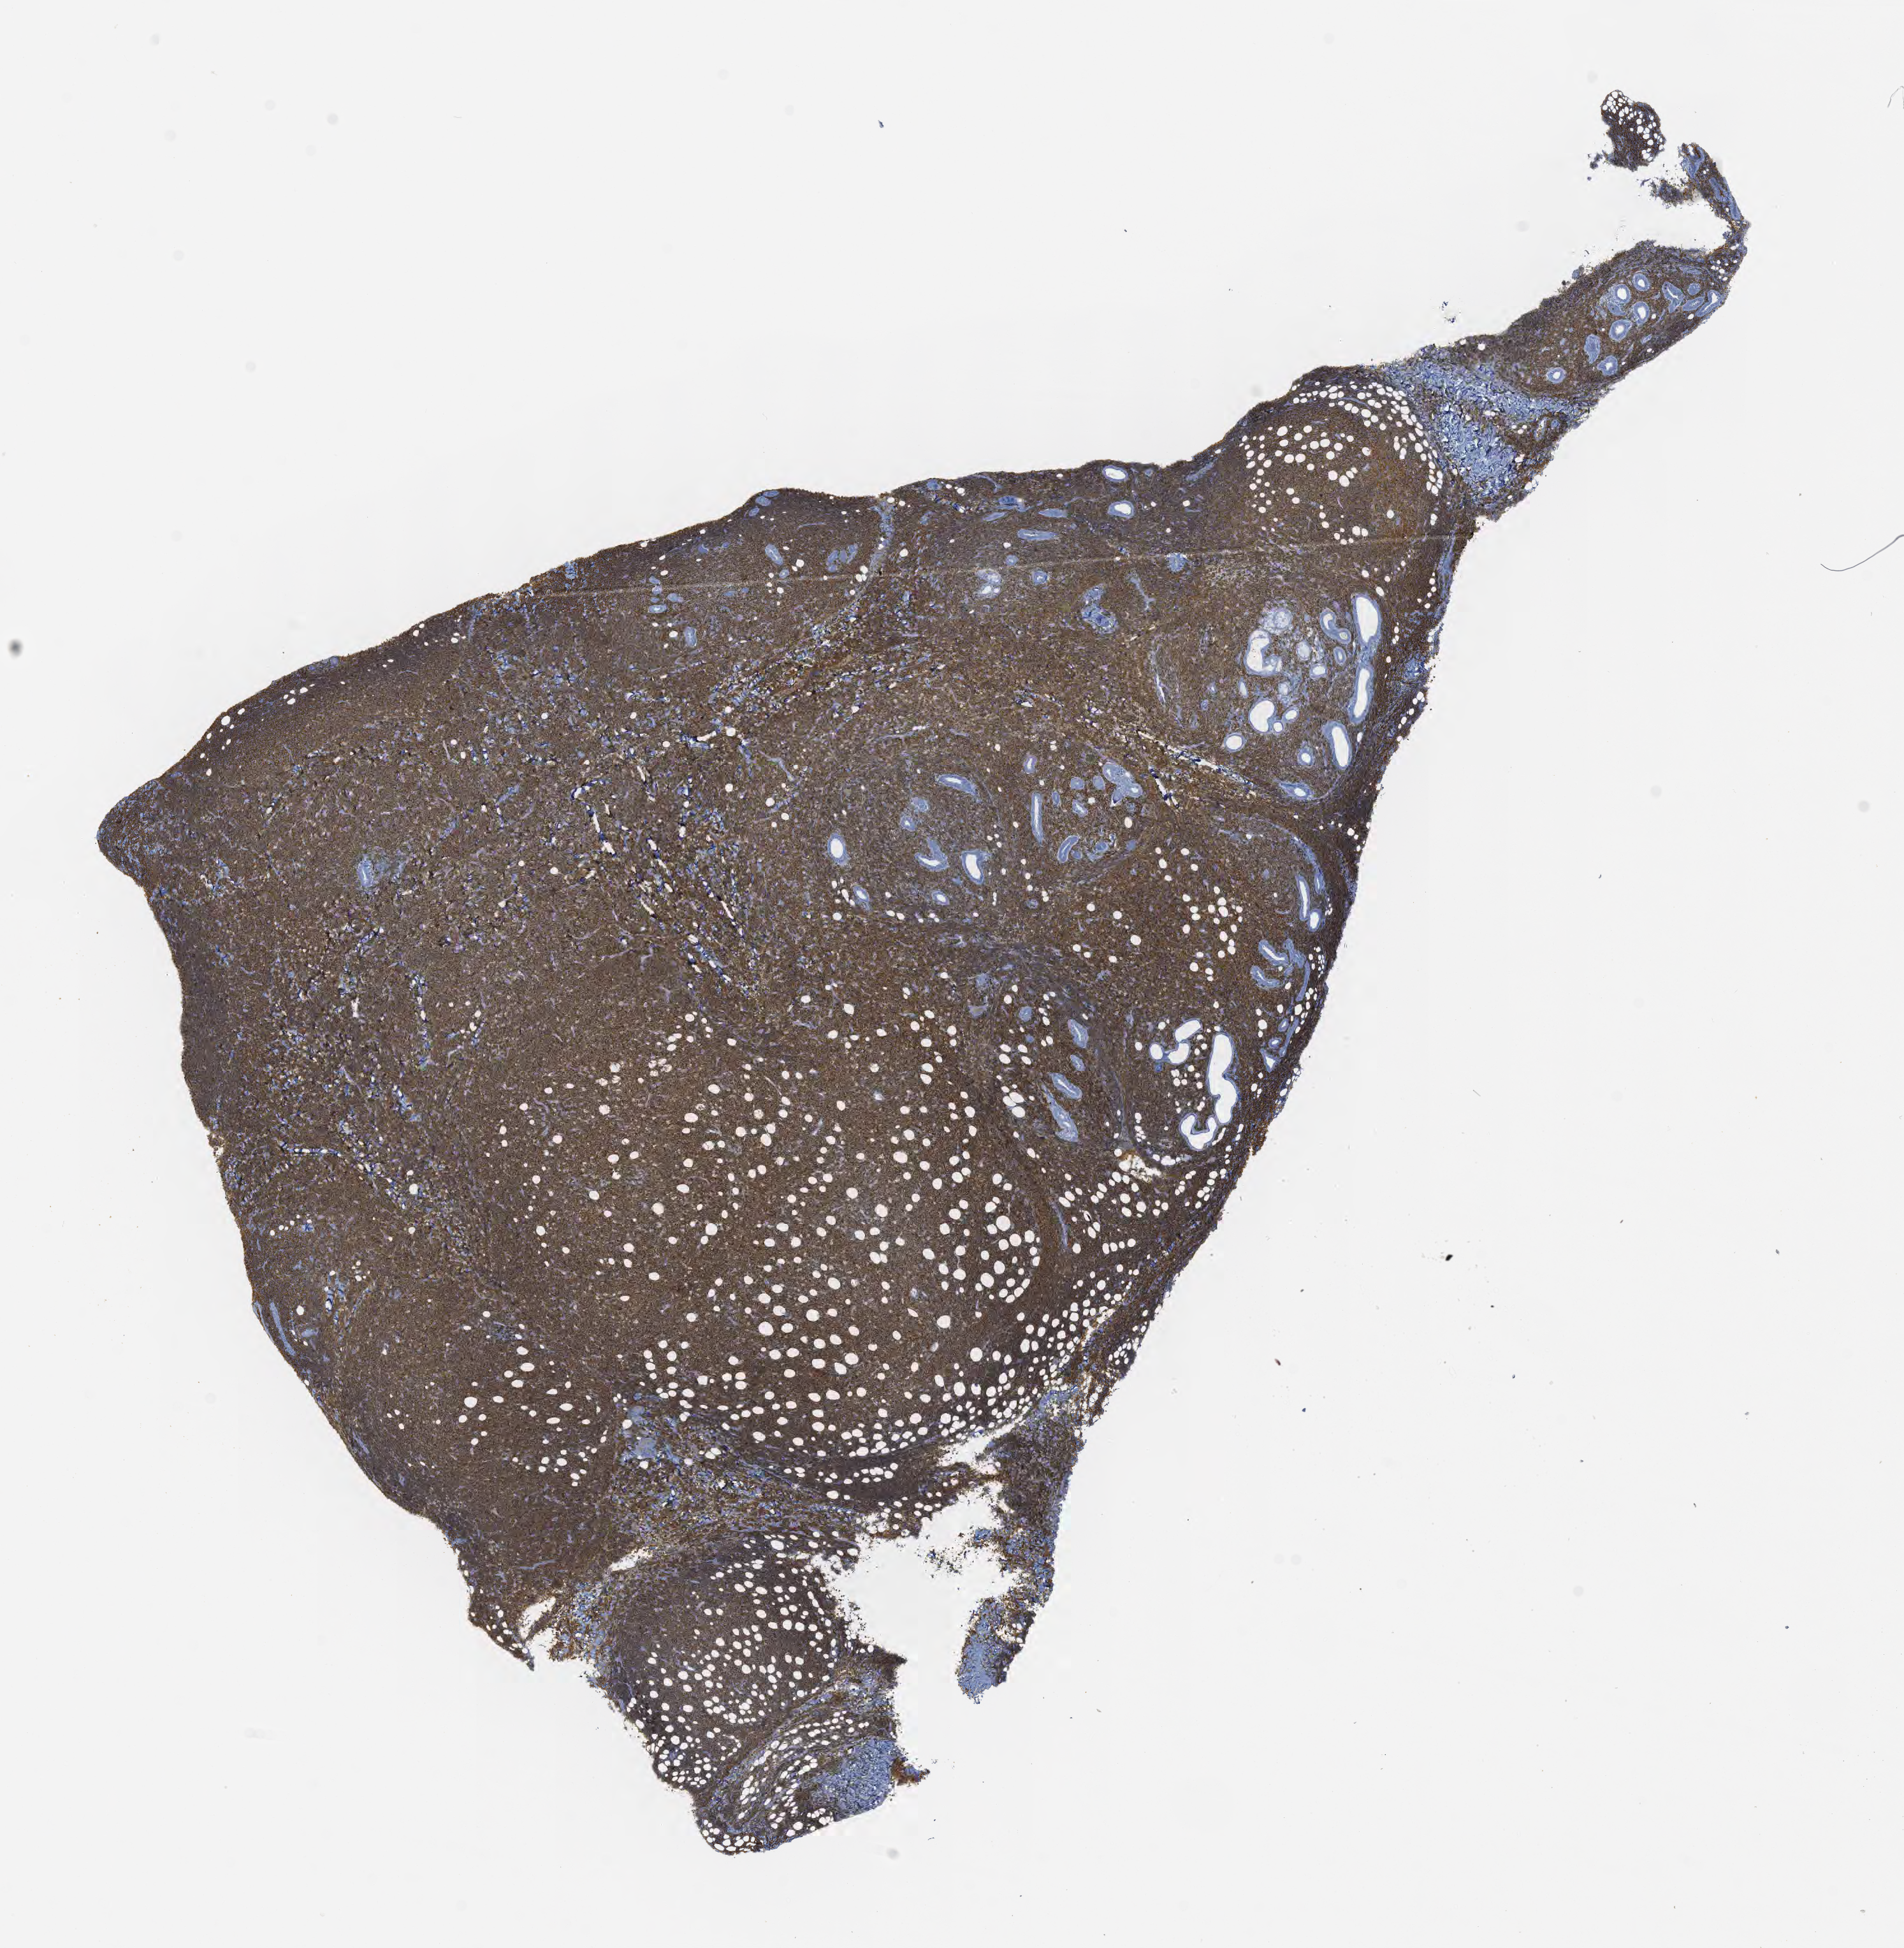
Whole-slide image, immunohistochemical stain for CD20 — whole scanned area (about 12.1 x 12.4 mm) shown as a low-resolution overview, specimen: tumor tissue. Patient male; age 46 years.
* histologic diagnosis: Burkitt lymphoma, NOS